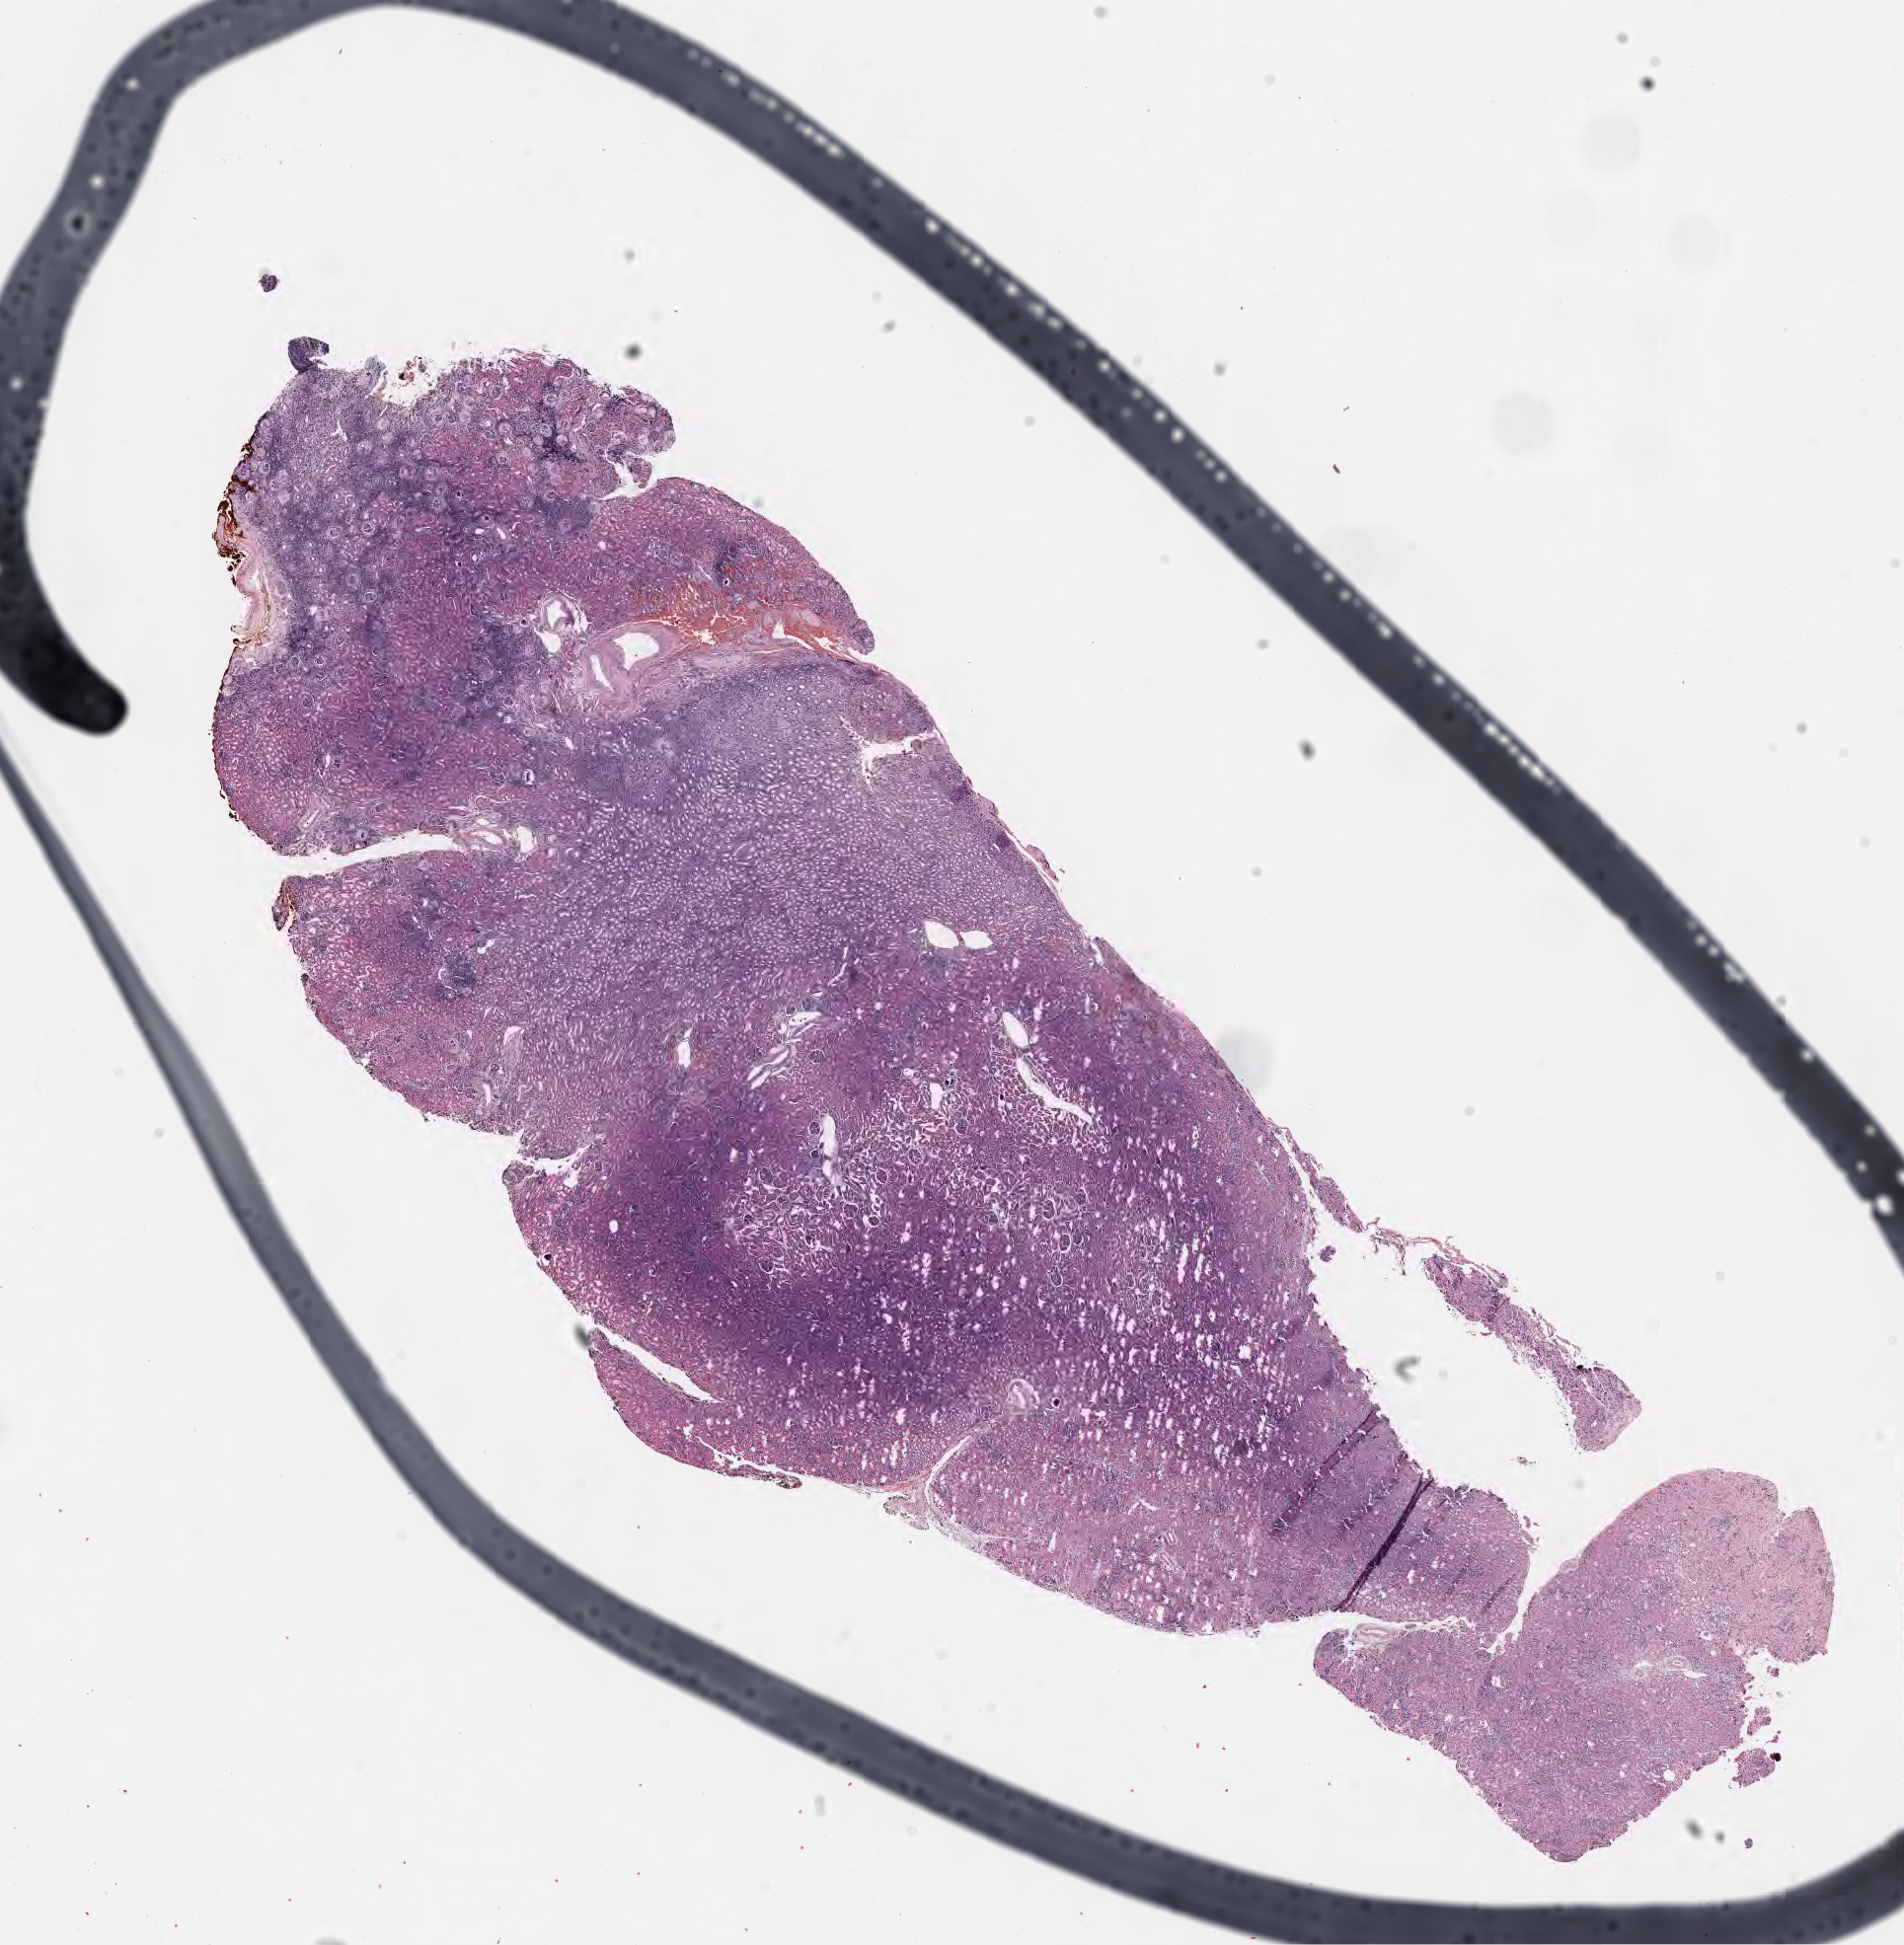
Whole-slide image, hematoxylin and eosin (H&E) stain — a low-resolution overview of the entire scanned area, about 15.6 x 15.9 mm; formalin-fixed, paraffin-embedded (FFPE) tissue; non-tumor (normal tissue) sample from a patient with nephroblastoma, NOS; site: kidney. Patient: female, age at initial diagnosis 3 years. Composition of this section per pathologist review: tumor cells 0%, tumor nuclei 0%, stromal cells 20%, necrosis 0%, normal cells 80%. Infiltration values recorded for this section: lymphocyte infiltration 25%, monocyte infiltration 2%, neutrophil infiltration 0%.
- this section: non-tumor tissue sample; the patient's diagnosis is given above